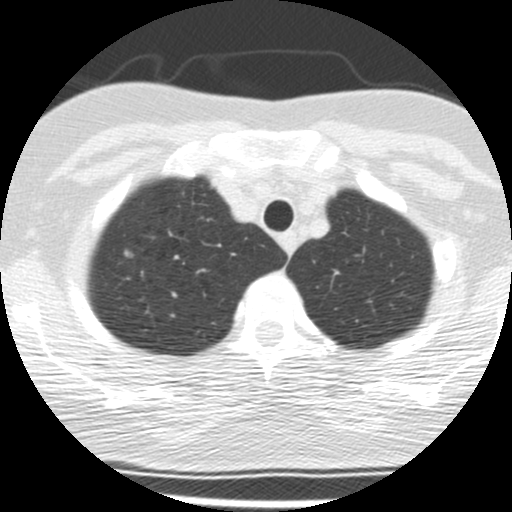
Low-dose screening chest CT, one axial slice. Slice 156 of 190 in the series (ordered by position). Reconstruction kernel STANDARD. 120 kVp. Lung window (W 1500 / L -600 HU). 2.5 mm slice thickness. 512 × 512 image matrix, field of view 274 × 274 mm.
Structures marked on this image (manually delineated by an expert):
- lesion 1 (tumor, upper lobe of right lung): bounding box <124,250,134,258> (left, top, right, bottom; pixels)